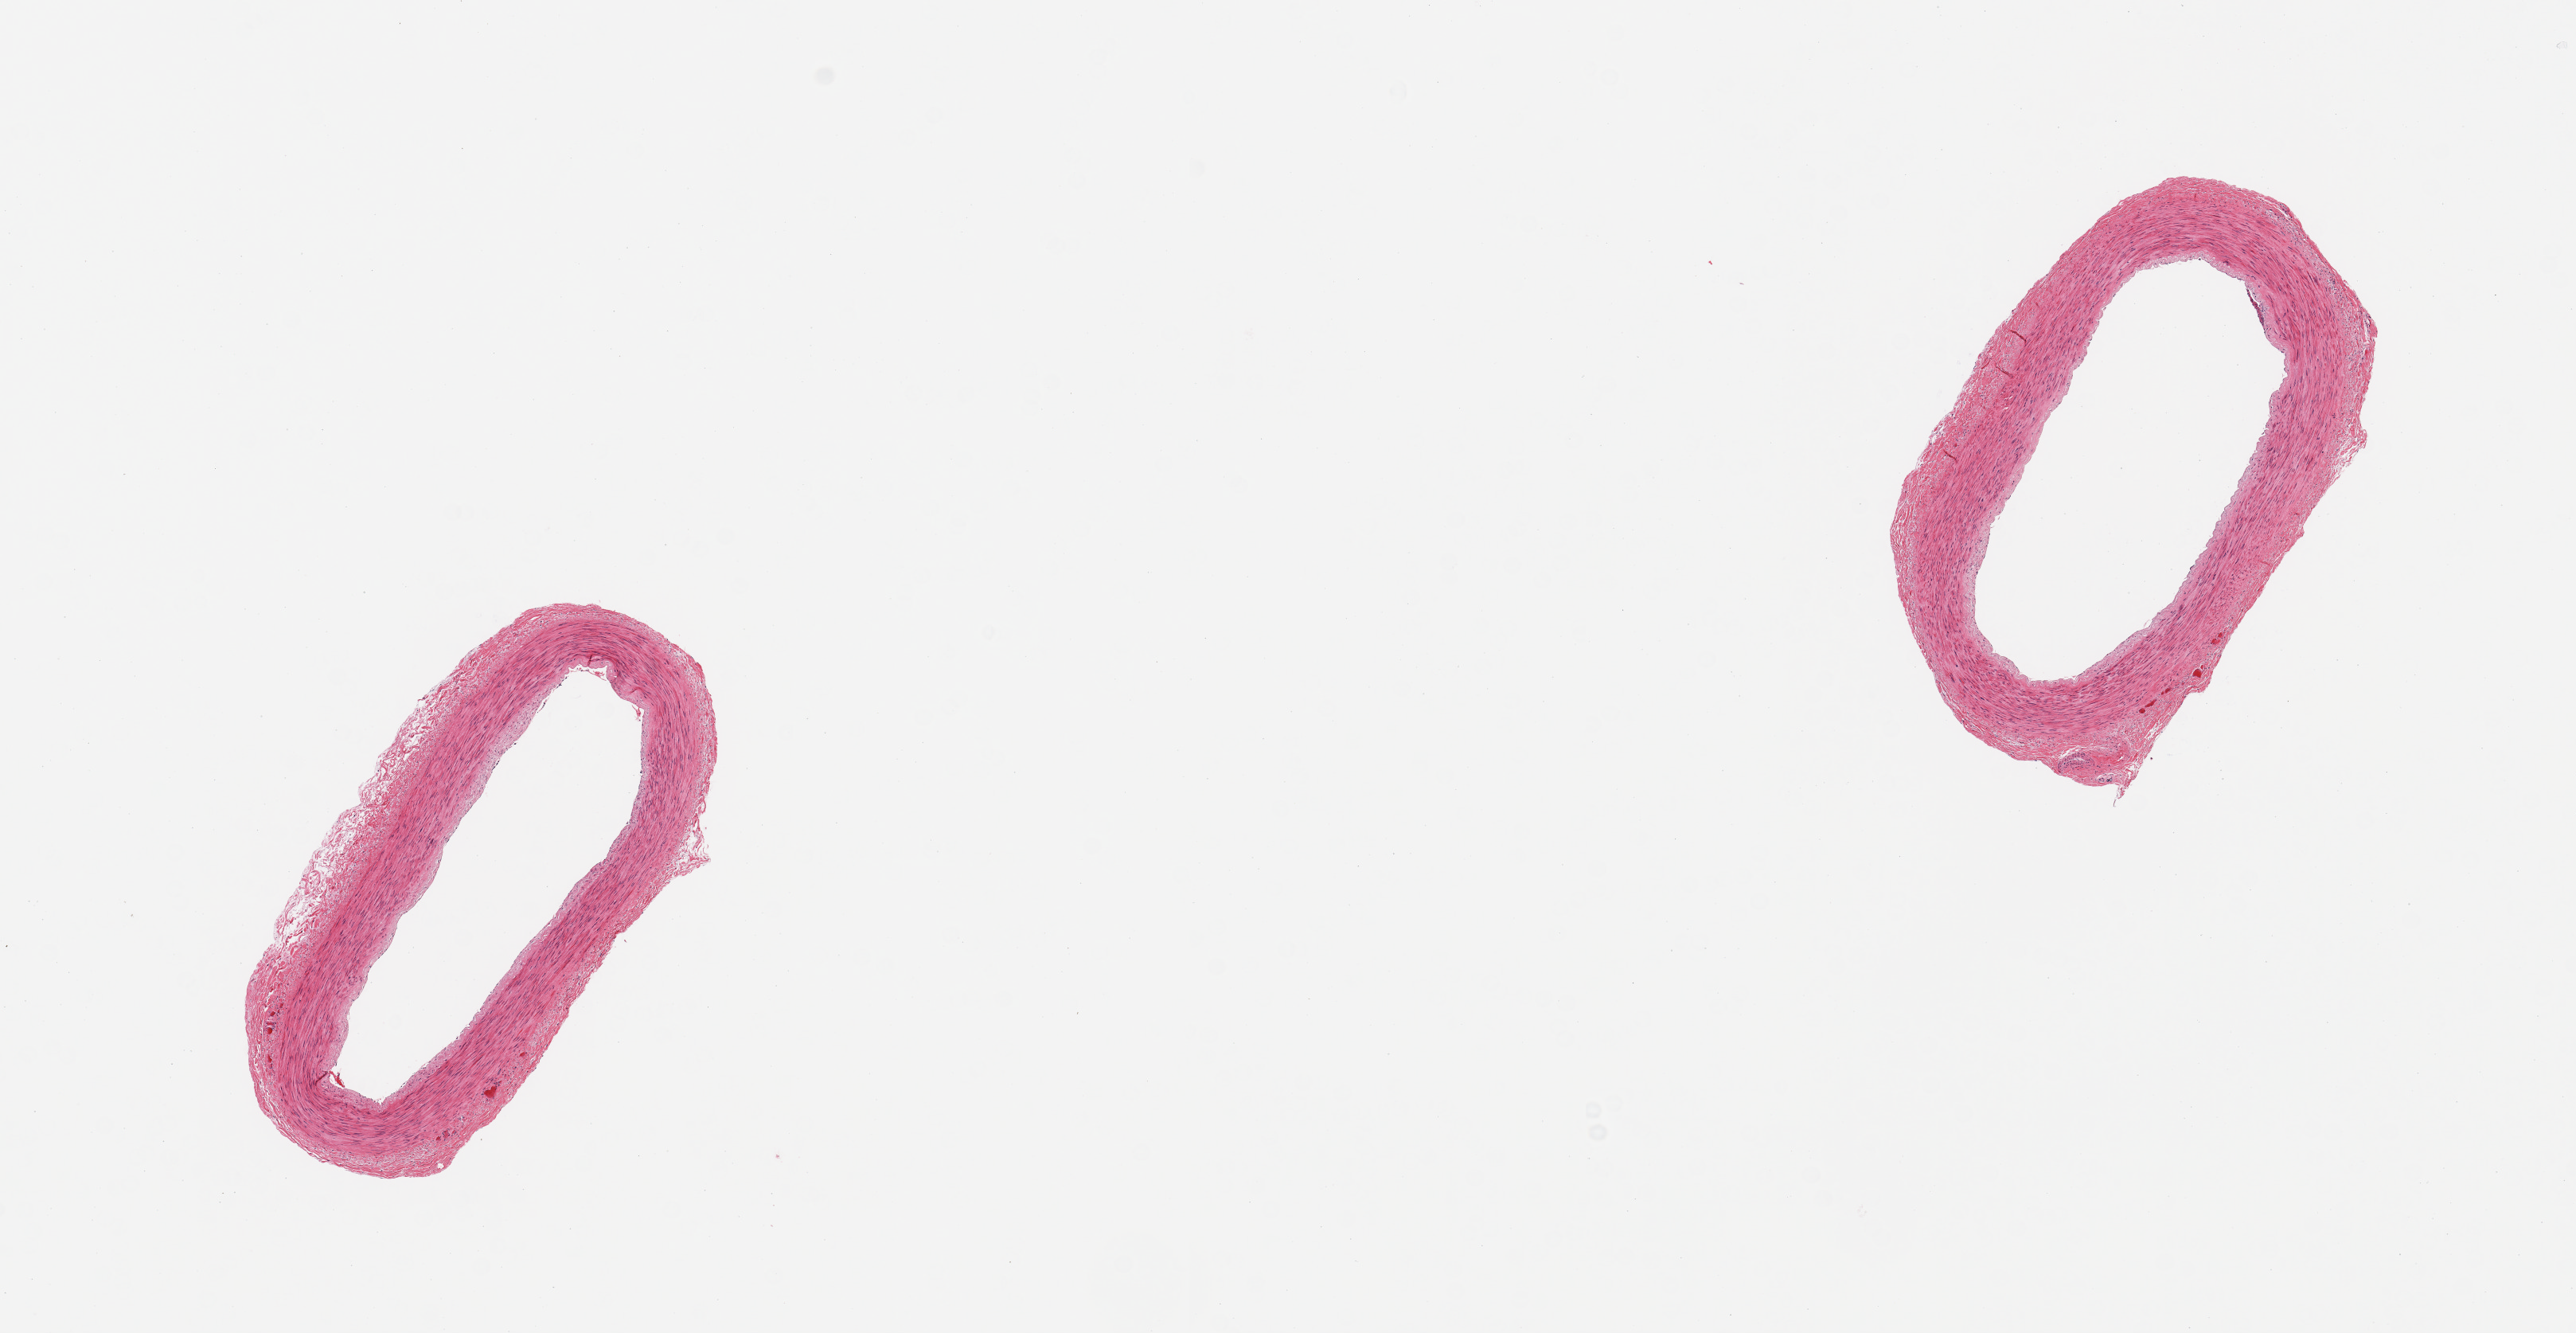
Whole-slide image, haematoxylin and eosin stain, brightfield — a low-resolution overview of the entire scanned area, about 12.8 x 6.6 mm. PAXgene-fixed, paraffin-embedded tissue. Section of tibial artery (target tissue). Tissue donor sample. Donor: female.
Pathologist's review note for this sample: 2 pieces; well trimmed; no lesions.